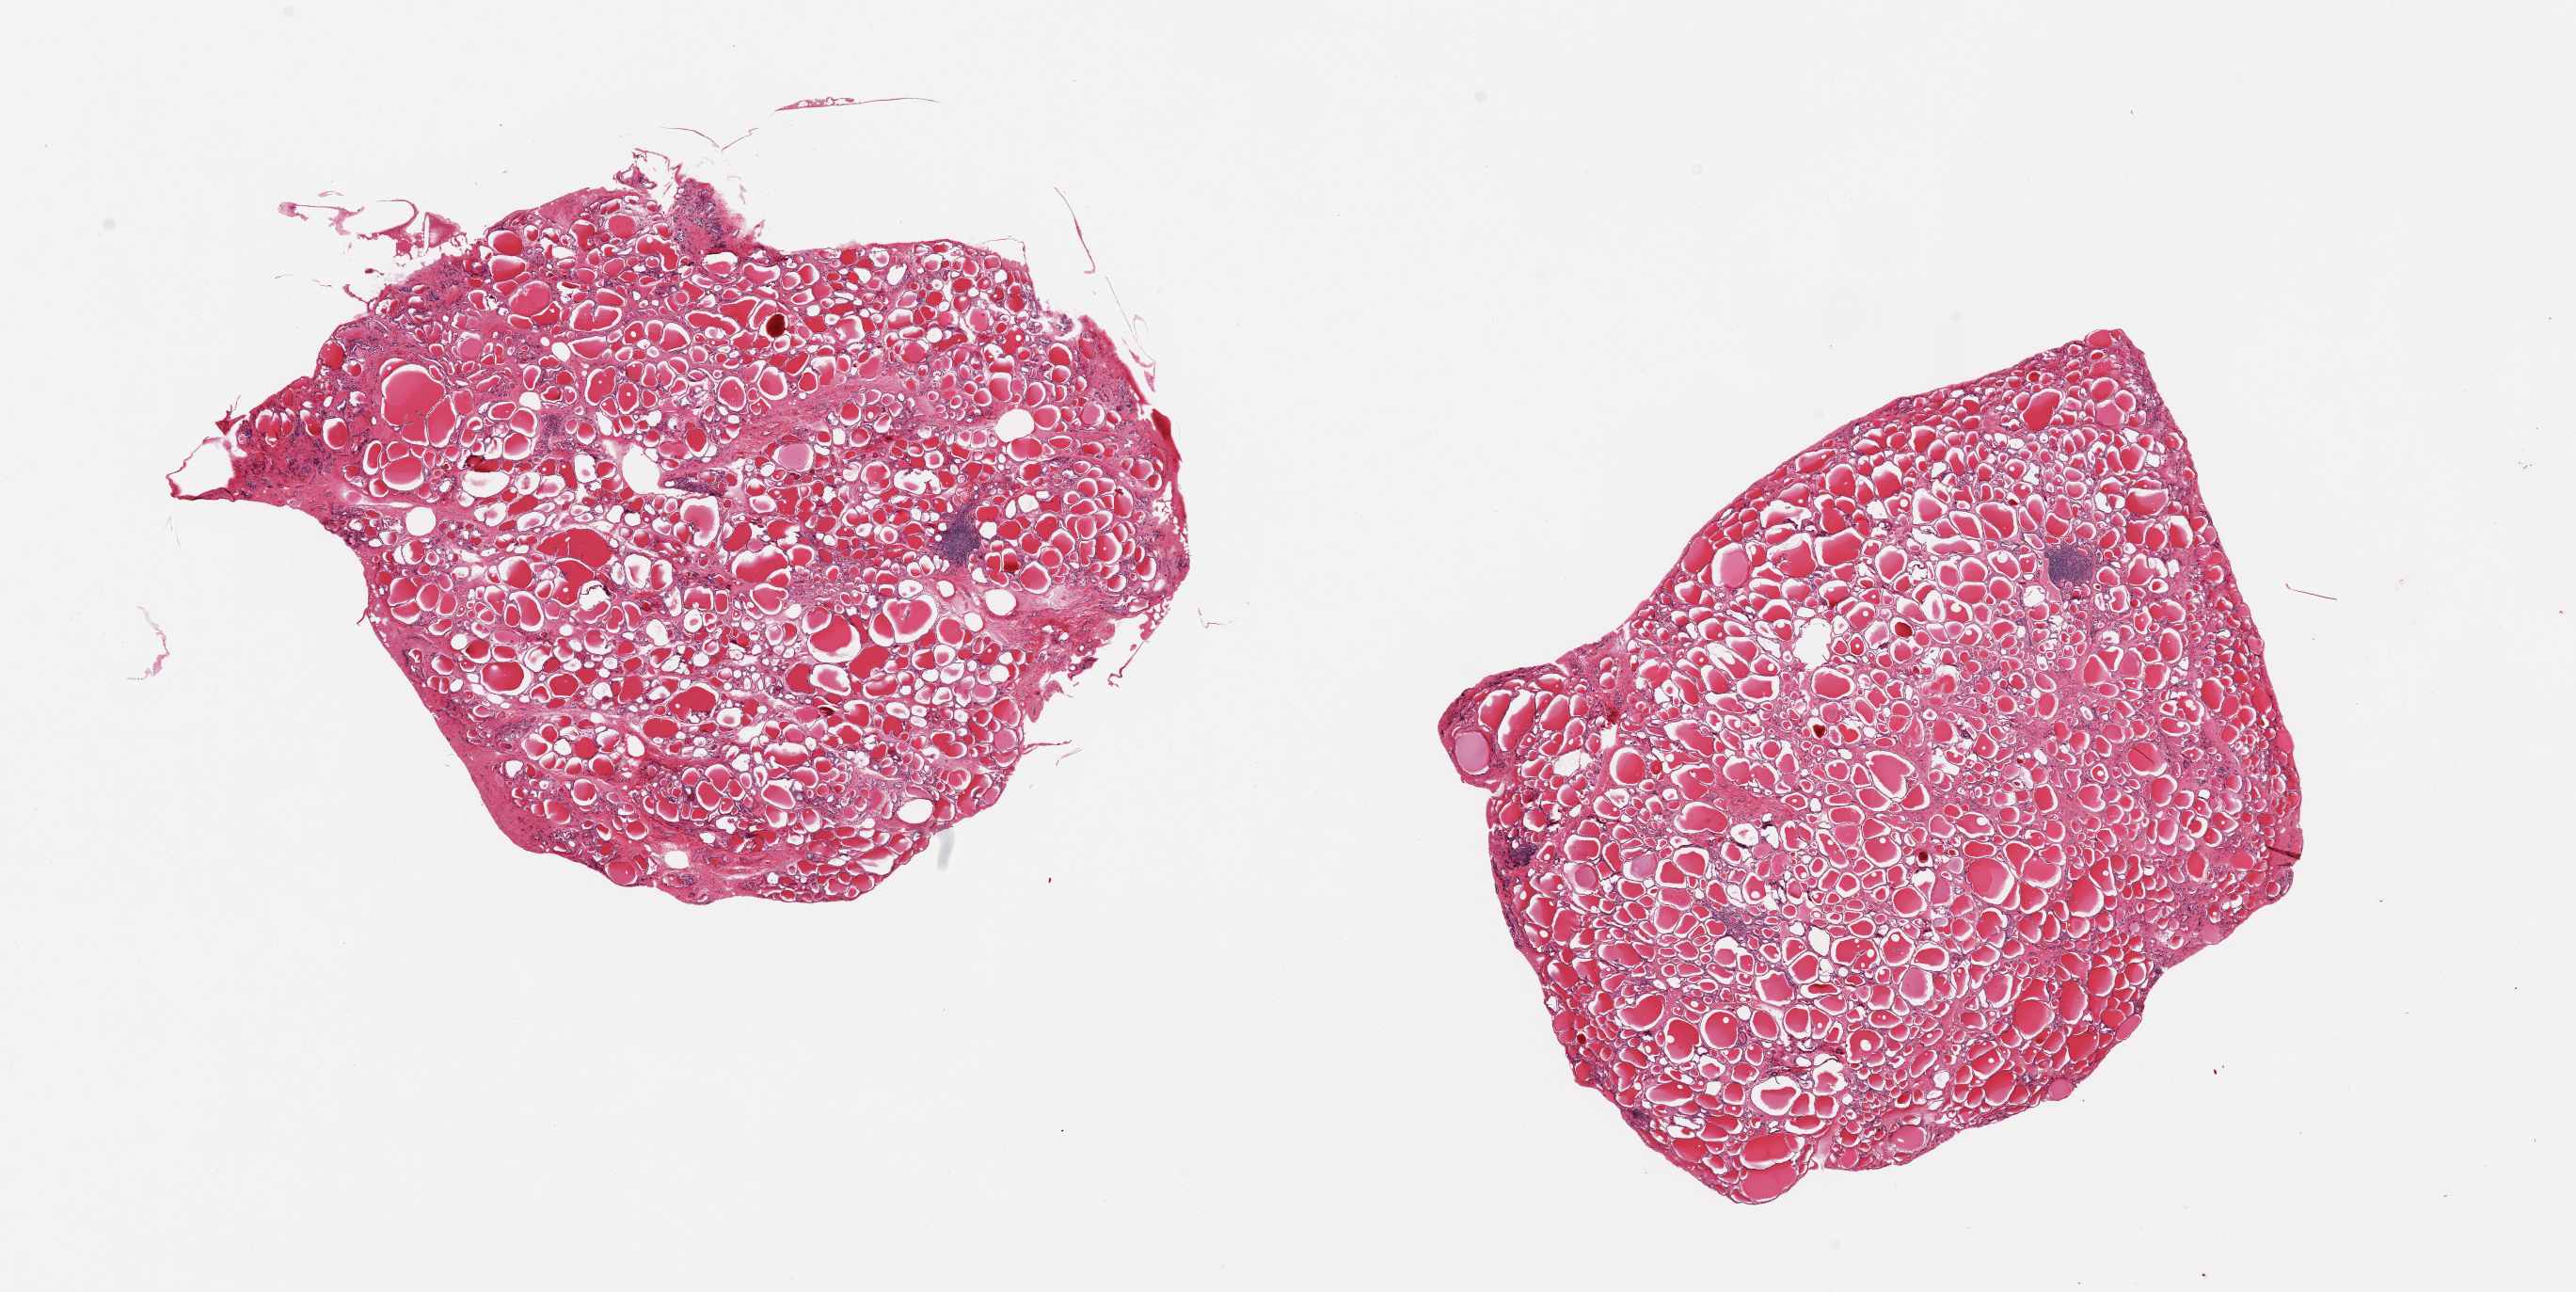
Whole-slide image, hematoxylin and eosin (H&E) stain — low-resolution overview of the scanned area, about 21.7 x 10.9 mm, PAXgene-fixed, paraffin-embedded tissue, section of thyroid (target tissue), donor tissue sample. Donor: male.
• pathologist's review note for this sample: 2 pieces, 2 small lymphcyitic aggregates